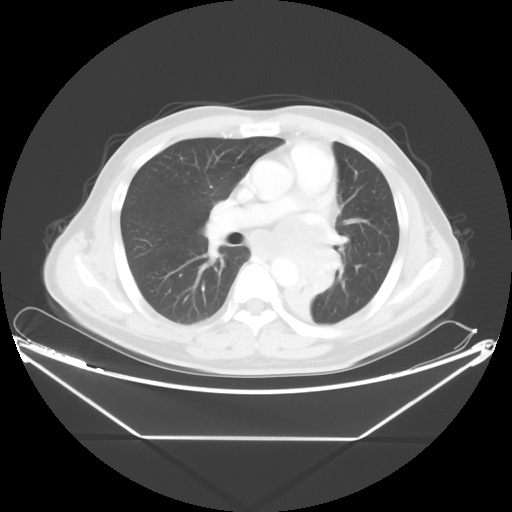
Chest CT, one axial slice. Slice 26 of 48 in the series (ordered by position). Reconstruction kernel STANDARD. Lung window (W 1500 / L -600 HU). 5 mm slice thickness. 512 × 512 image matrix, field of view 438 × 438 mm. Patient: male, 58 years. From the clinical record (not read from this slice): clinical TNM (as recorded): T3 N3 M0.
Annotated regions visible in this slice (bounding box drawn by a radiologist):
- lung tumour (recorded histology: squamous cell carcinoma): bounding box [x1, y1, x2, y2] px = [287, 255, 328, 324]